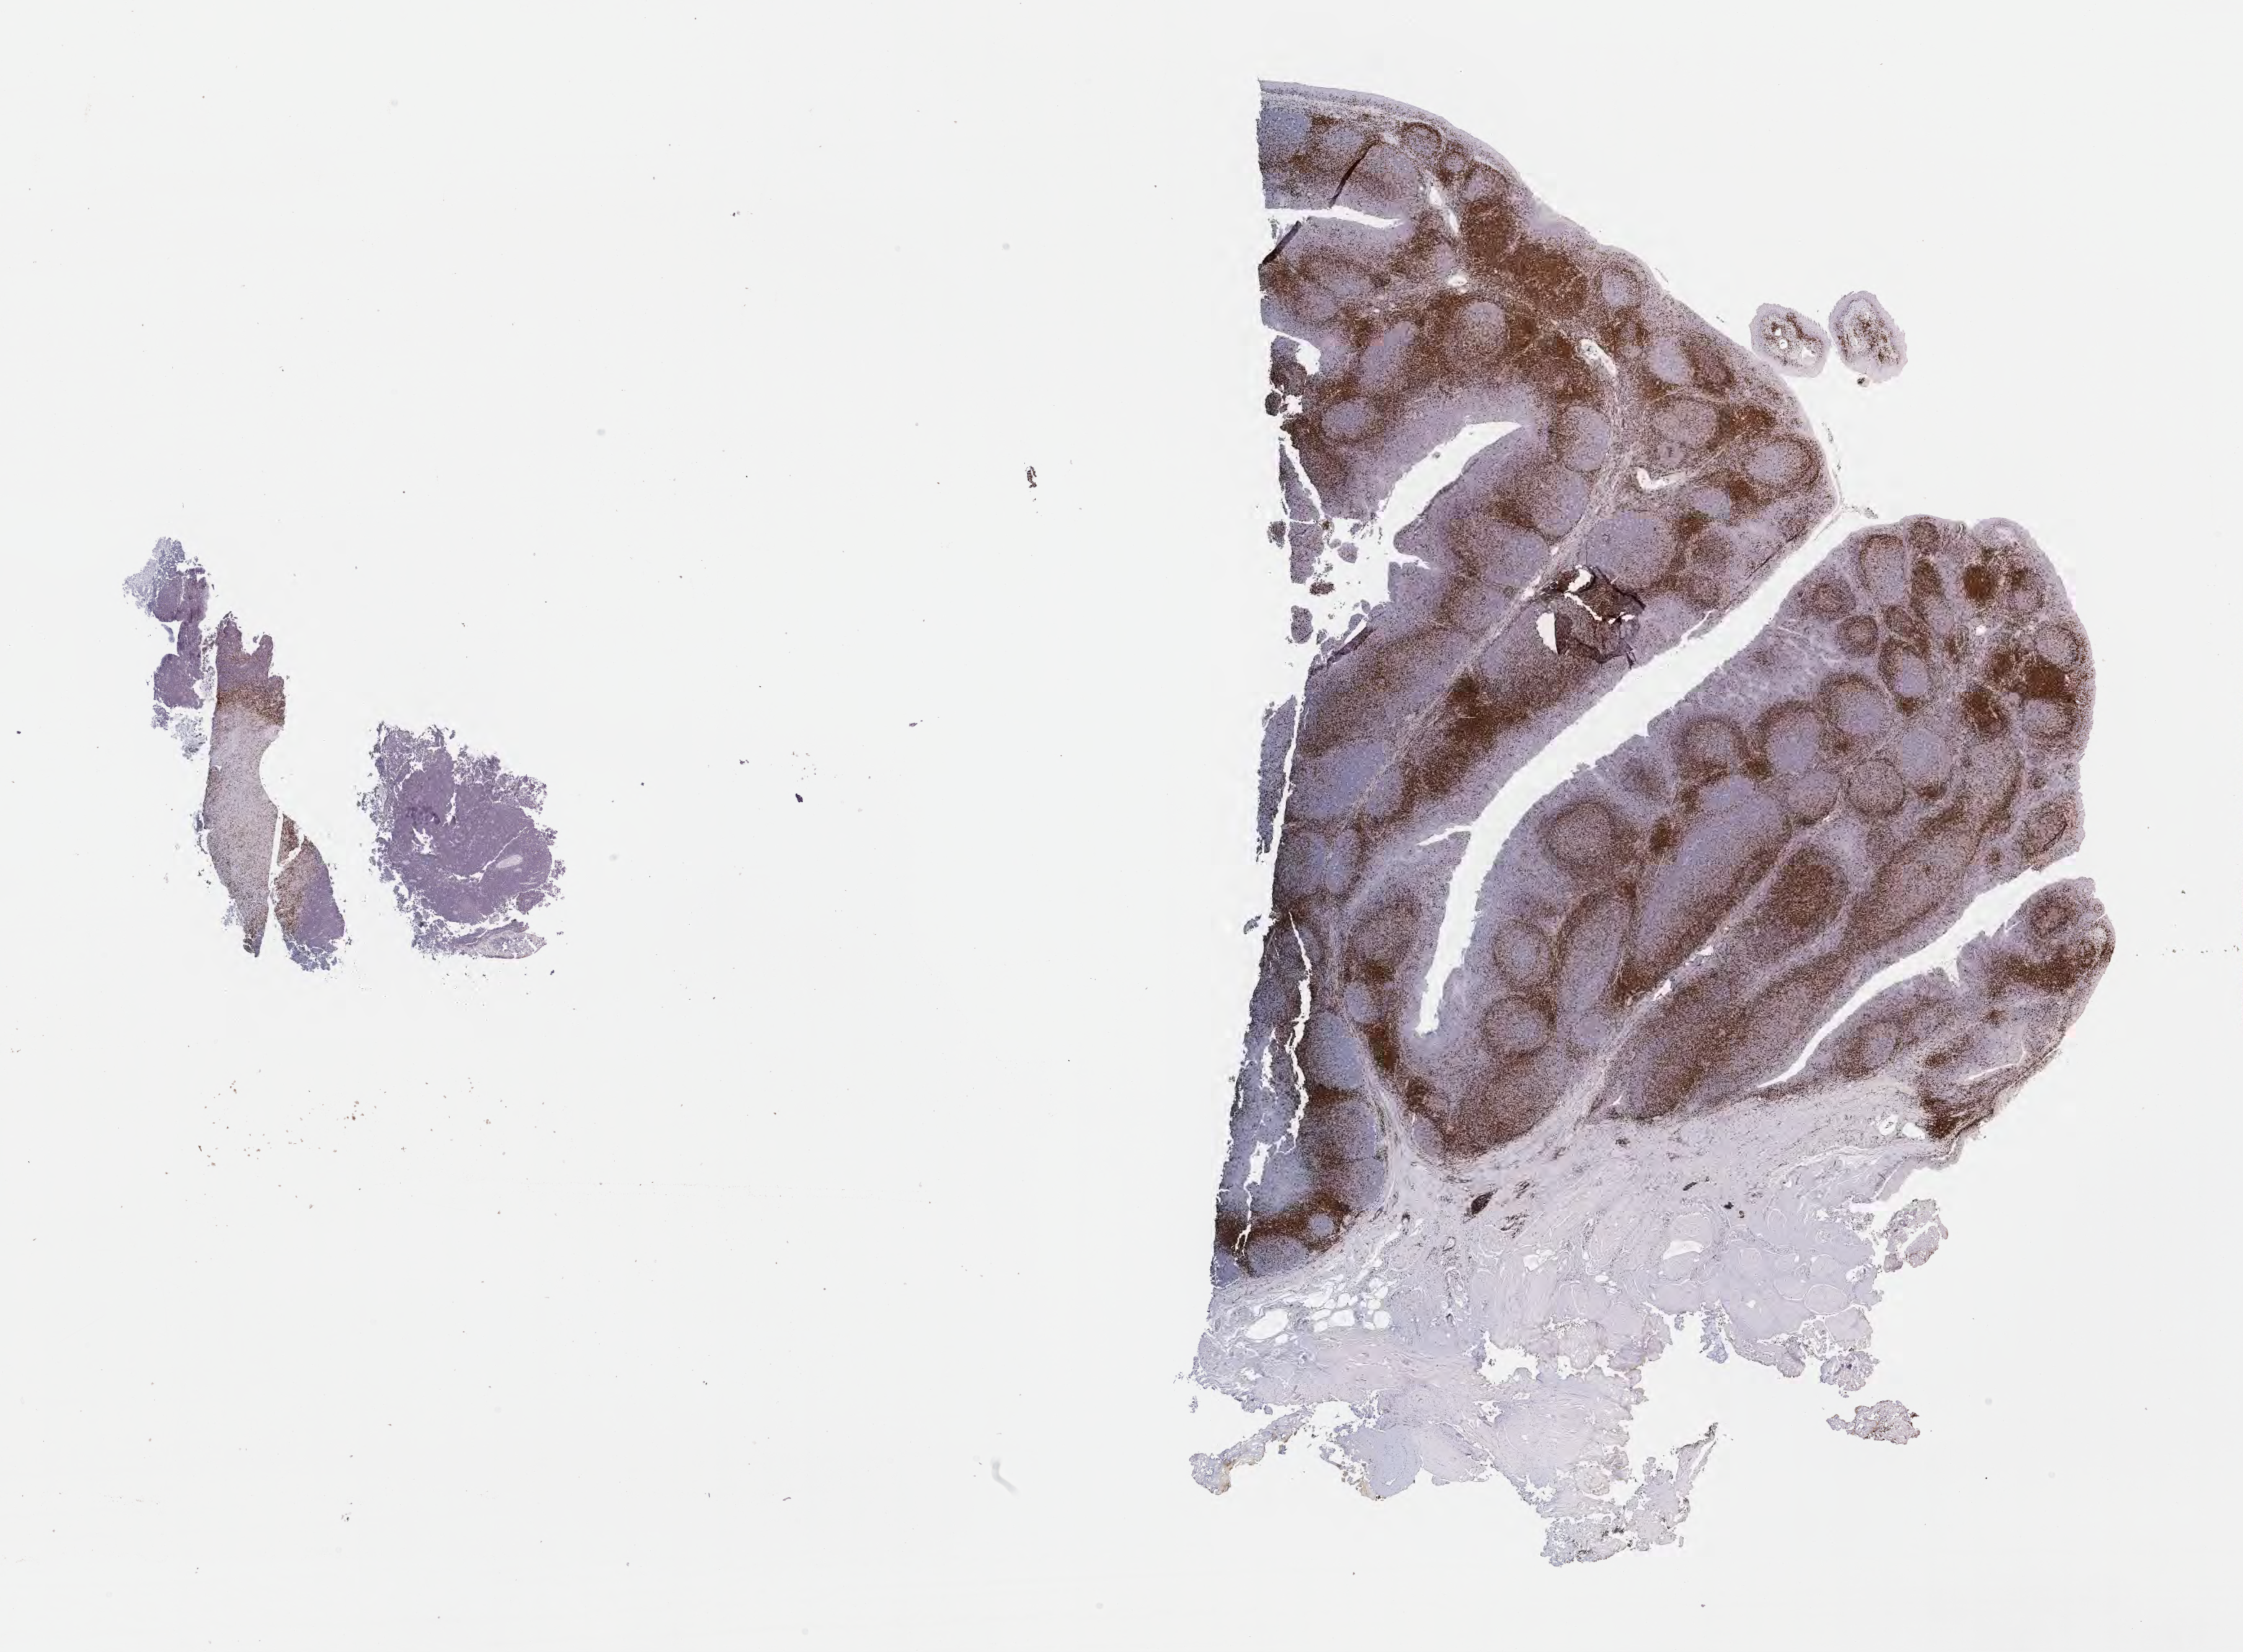
IHC for CD3, whole-slide image, low-resolution overview of the scanned area, about 25.2 x 18.5 mm. Tumor tissue. Site: cranium. Male, age 4 years at initial diagnosis.
Histologic diagnosis: Burkitt lymphoma, NOS.